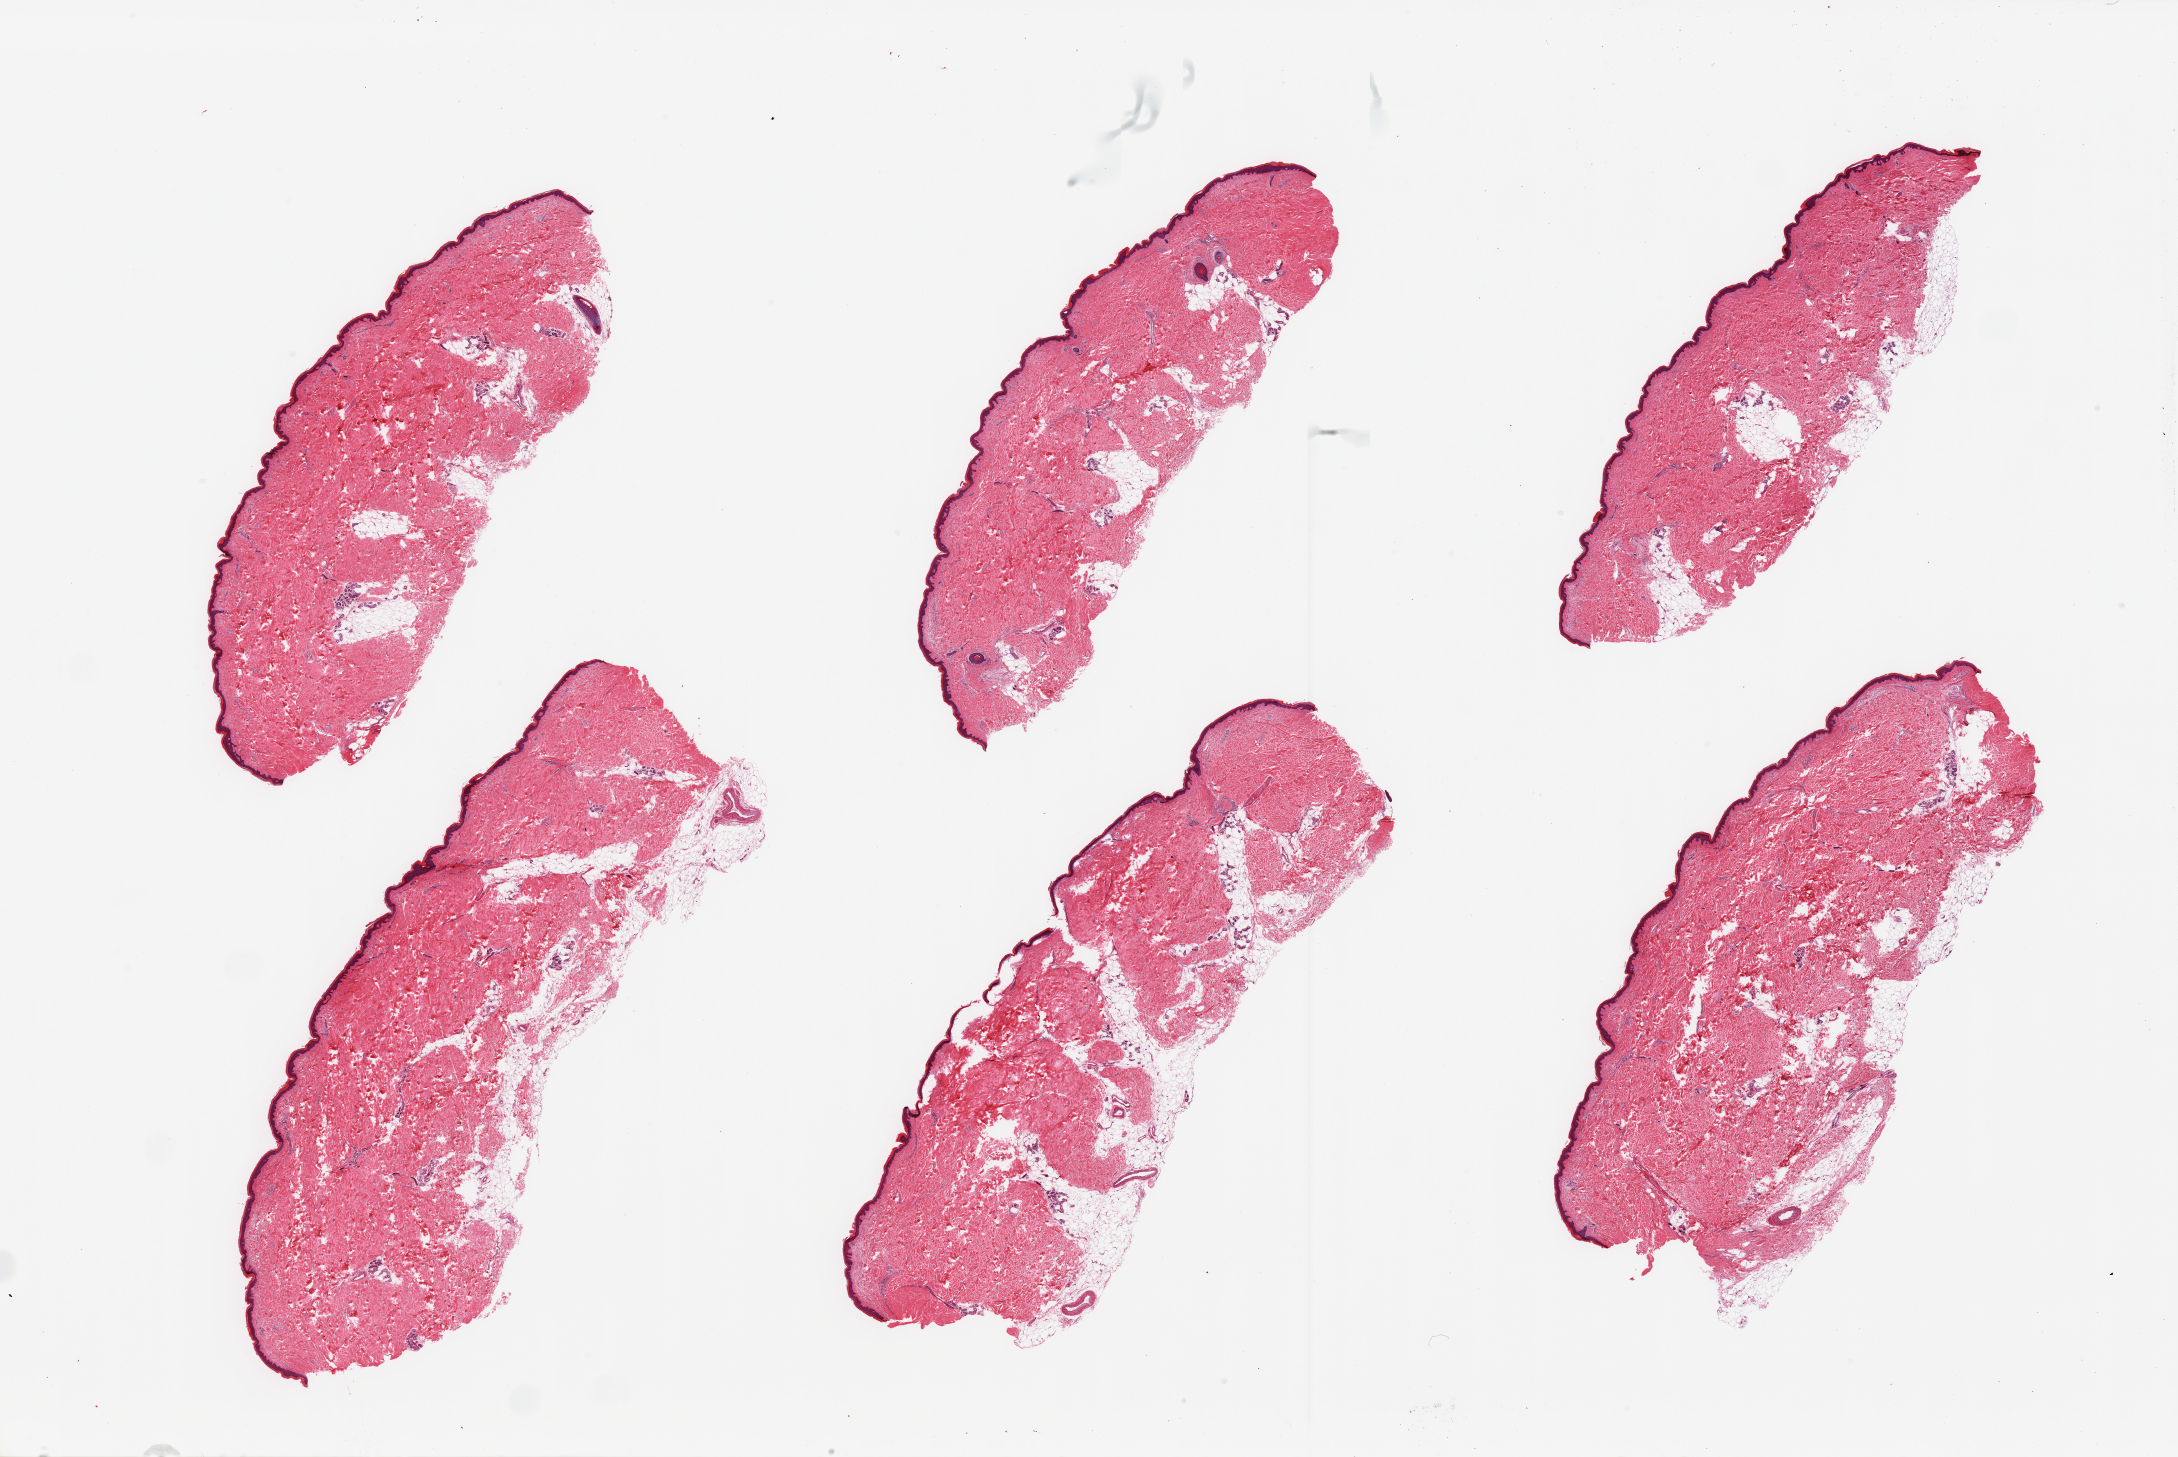
Whole-slide image, hematoxylin and eosin (H&E) stain, brightfield, low-resolution overview of the scanned area, about 34.5 x 23.0 mm (from a 20x scan); PAXgene-fixed paraffin-embedded (PFPE) section; target tissue: skin of lower leg; donor tissue sample. Donor sex: male.
Pathologist's review note for this sample: 6 pieces; 5% to 20% internal/external fat, mostly periadnexal; epidermis ~40 micron thick; one piece with empty spaces mostly subepidermal and epidermal gap.